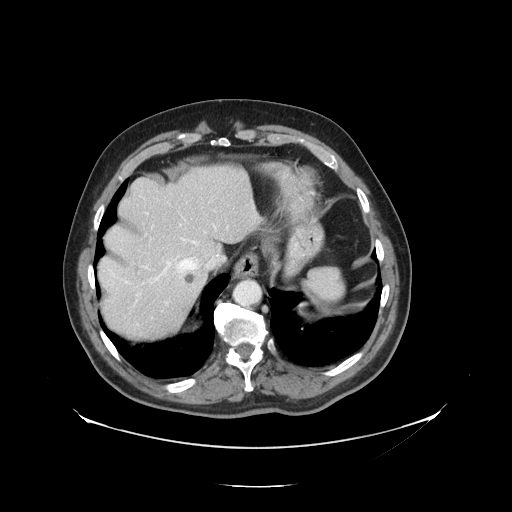
Contrast-enhanced abdominal CT, one axial slice. Position 111 of 138 along the scan axis. Intravenous contrast given. Soft-tissue window (W 400 / L 40 HU). 2.5 mm slice thickness. 512 × 512 image matrix, field of view 497 × 497 mm. Male patient, age 77 years. From the clinical record (not read from this slice): diagnosis: colorectal cancer liver metastases, imaged before liver resection; multiple liver metastases: no.
Structures marked on this image (manually delineated by an expert):
- hepatic veins: bounding box (x1, y1, x2, y2) in pixels: (142, 200, 217, 285)
- liver: (99, 167, 256, 339)
- planned liver remnant (the part of the liver to remain after resection): (99, 167, 257, 290)
- portal vein (with intrahepatic branches): (164, 188, 214, 305)
- liver metastasis: (185, 274, 196, 284)